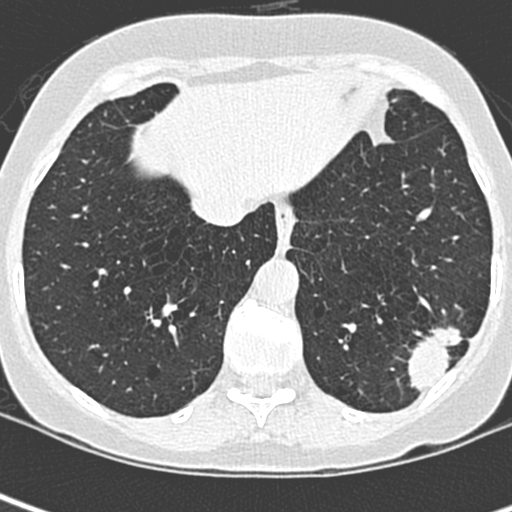
Low-dose screening chest CT, one axial slice. Slice 74 of 252 in the series (ordered by position). 120 kVp. Lung window (W 1500 / L -600 HU). 1.3 mm slice thickness. 512 × 512 image matrix, field of view 271 × 271 mm.
Structures marked on this image (outlined manually by an expert reader):
- lesion 1 (tumor, lower lobe of left lung): bounding box <407,326,463,392> (left, top, right, bottom; pixels)